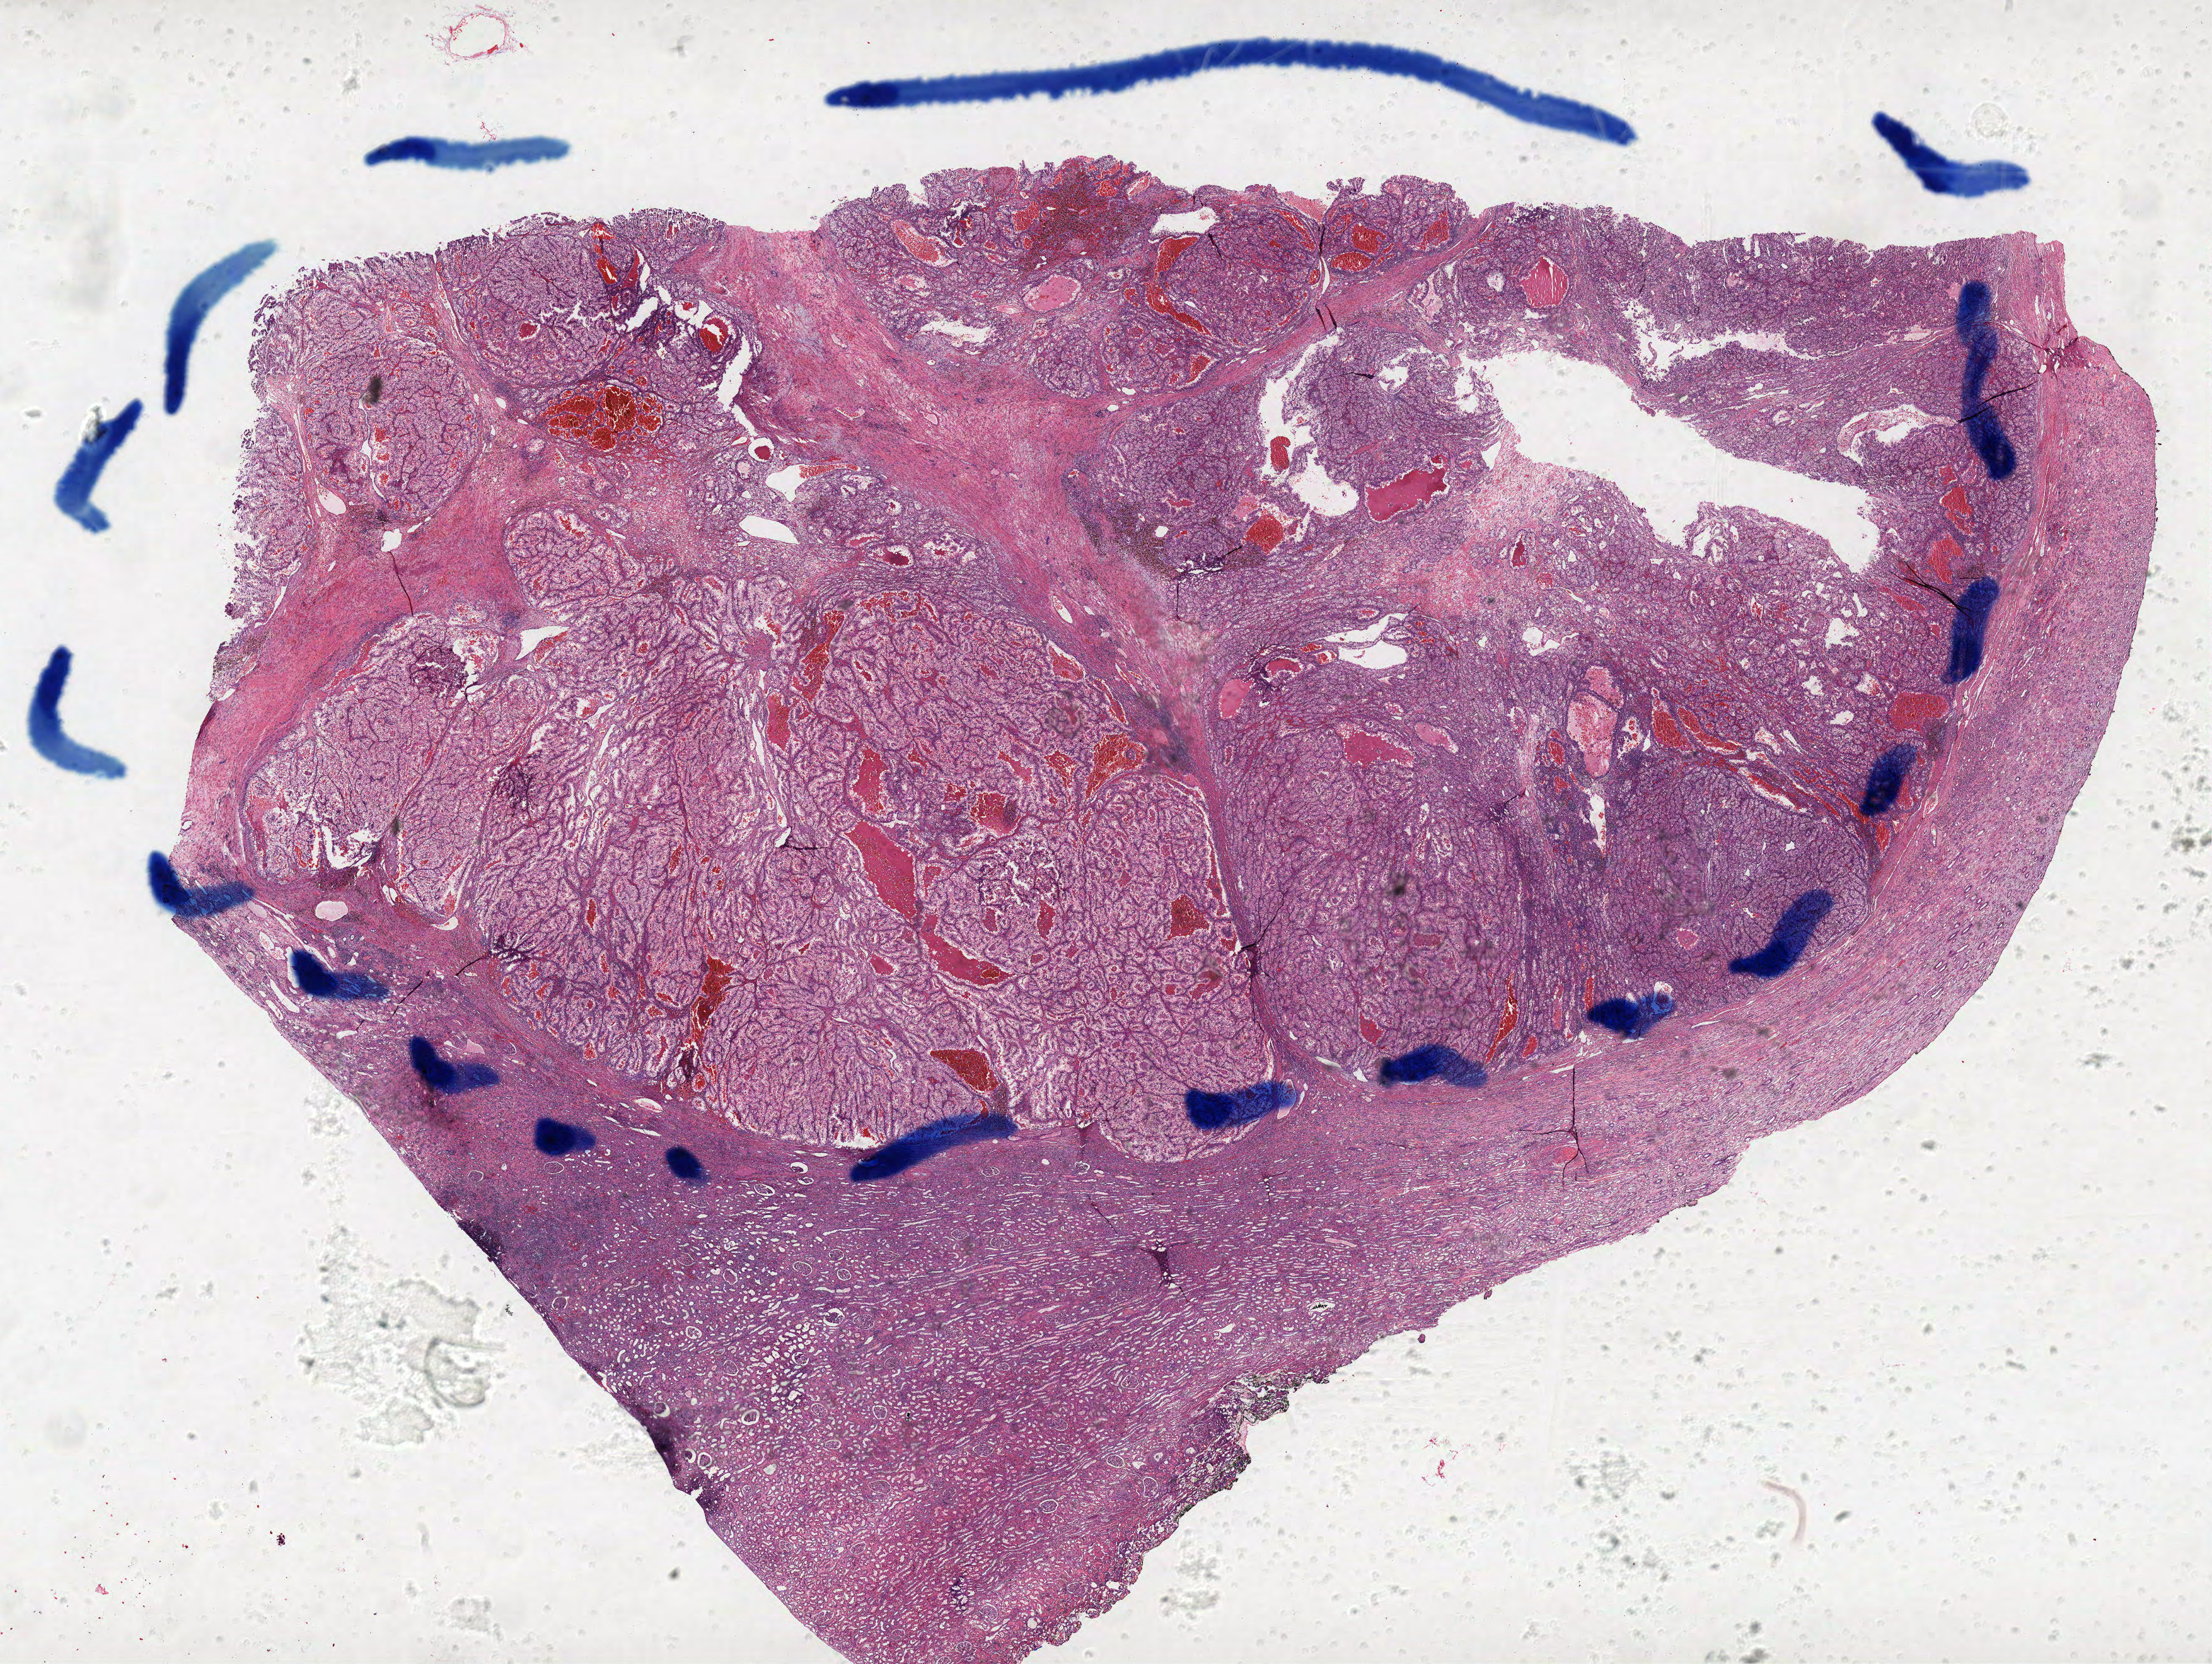
Digitized H&E-stained tissue section (whole slide), low-resolution overview of the scanned area, about 28.1 x 21.1 mm (from a 40x scan), formalin-fixed paraffin-embedded (FFPE) diagnostic section, primary tumour sample from the kidney. Patient: male, age at initial diagnosis 49 years. Histologic grade: G3 (poorly differentiated).
Laterality: right. AJCC pathologic stage: I. Diagnosis: Clear cell adenocarcinoma, NOS.